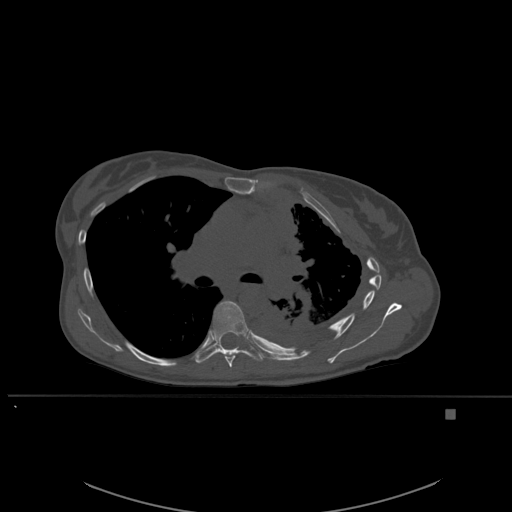
CT including the spine, one axial slice; bone window (W 1800 / L 400 HU); 512 × 512 image matrix, field of view 440 × 440 mm. Female patient, age 45 years. From the clinical record (not read from this slice): primary cancer: lung.
Structures marked on this image (semi-automatically segmented with operator editing):
- T6 vertebra: bounding box <224,355,235,368> (left, top, right, bottom; pixels)
- T7 vertebra: <196,301,267,364>